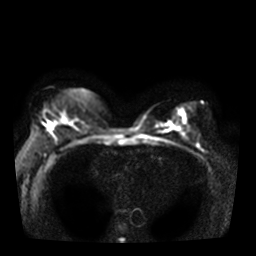
Breast MRI, one axial slice; slice 17 of 36 in the series (ordered by position); diffusion-weighted series; image 2 of 4 stored at this slice position (different b-values; order by instance number); 3 T; 256 × 256 image matrix. Female patient.
Outlined on this slice (expert manual segmentation):
- tumour on diffusion-weighted imaging: bounding box (x1, y1, x2, y2) in pixels: (68, 121, 74, 127)